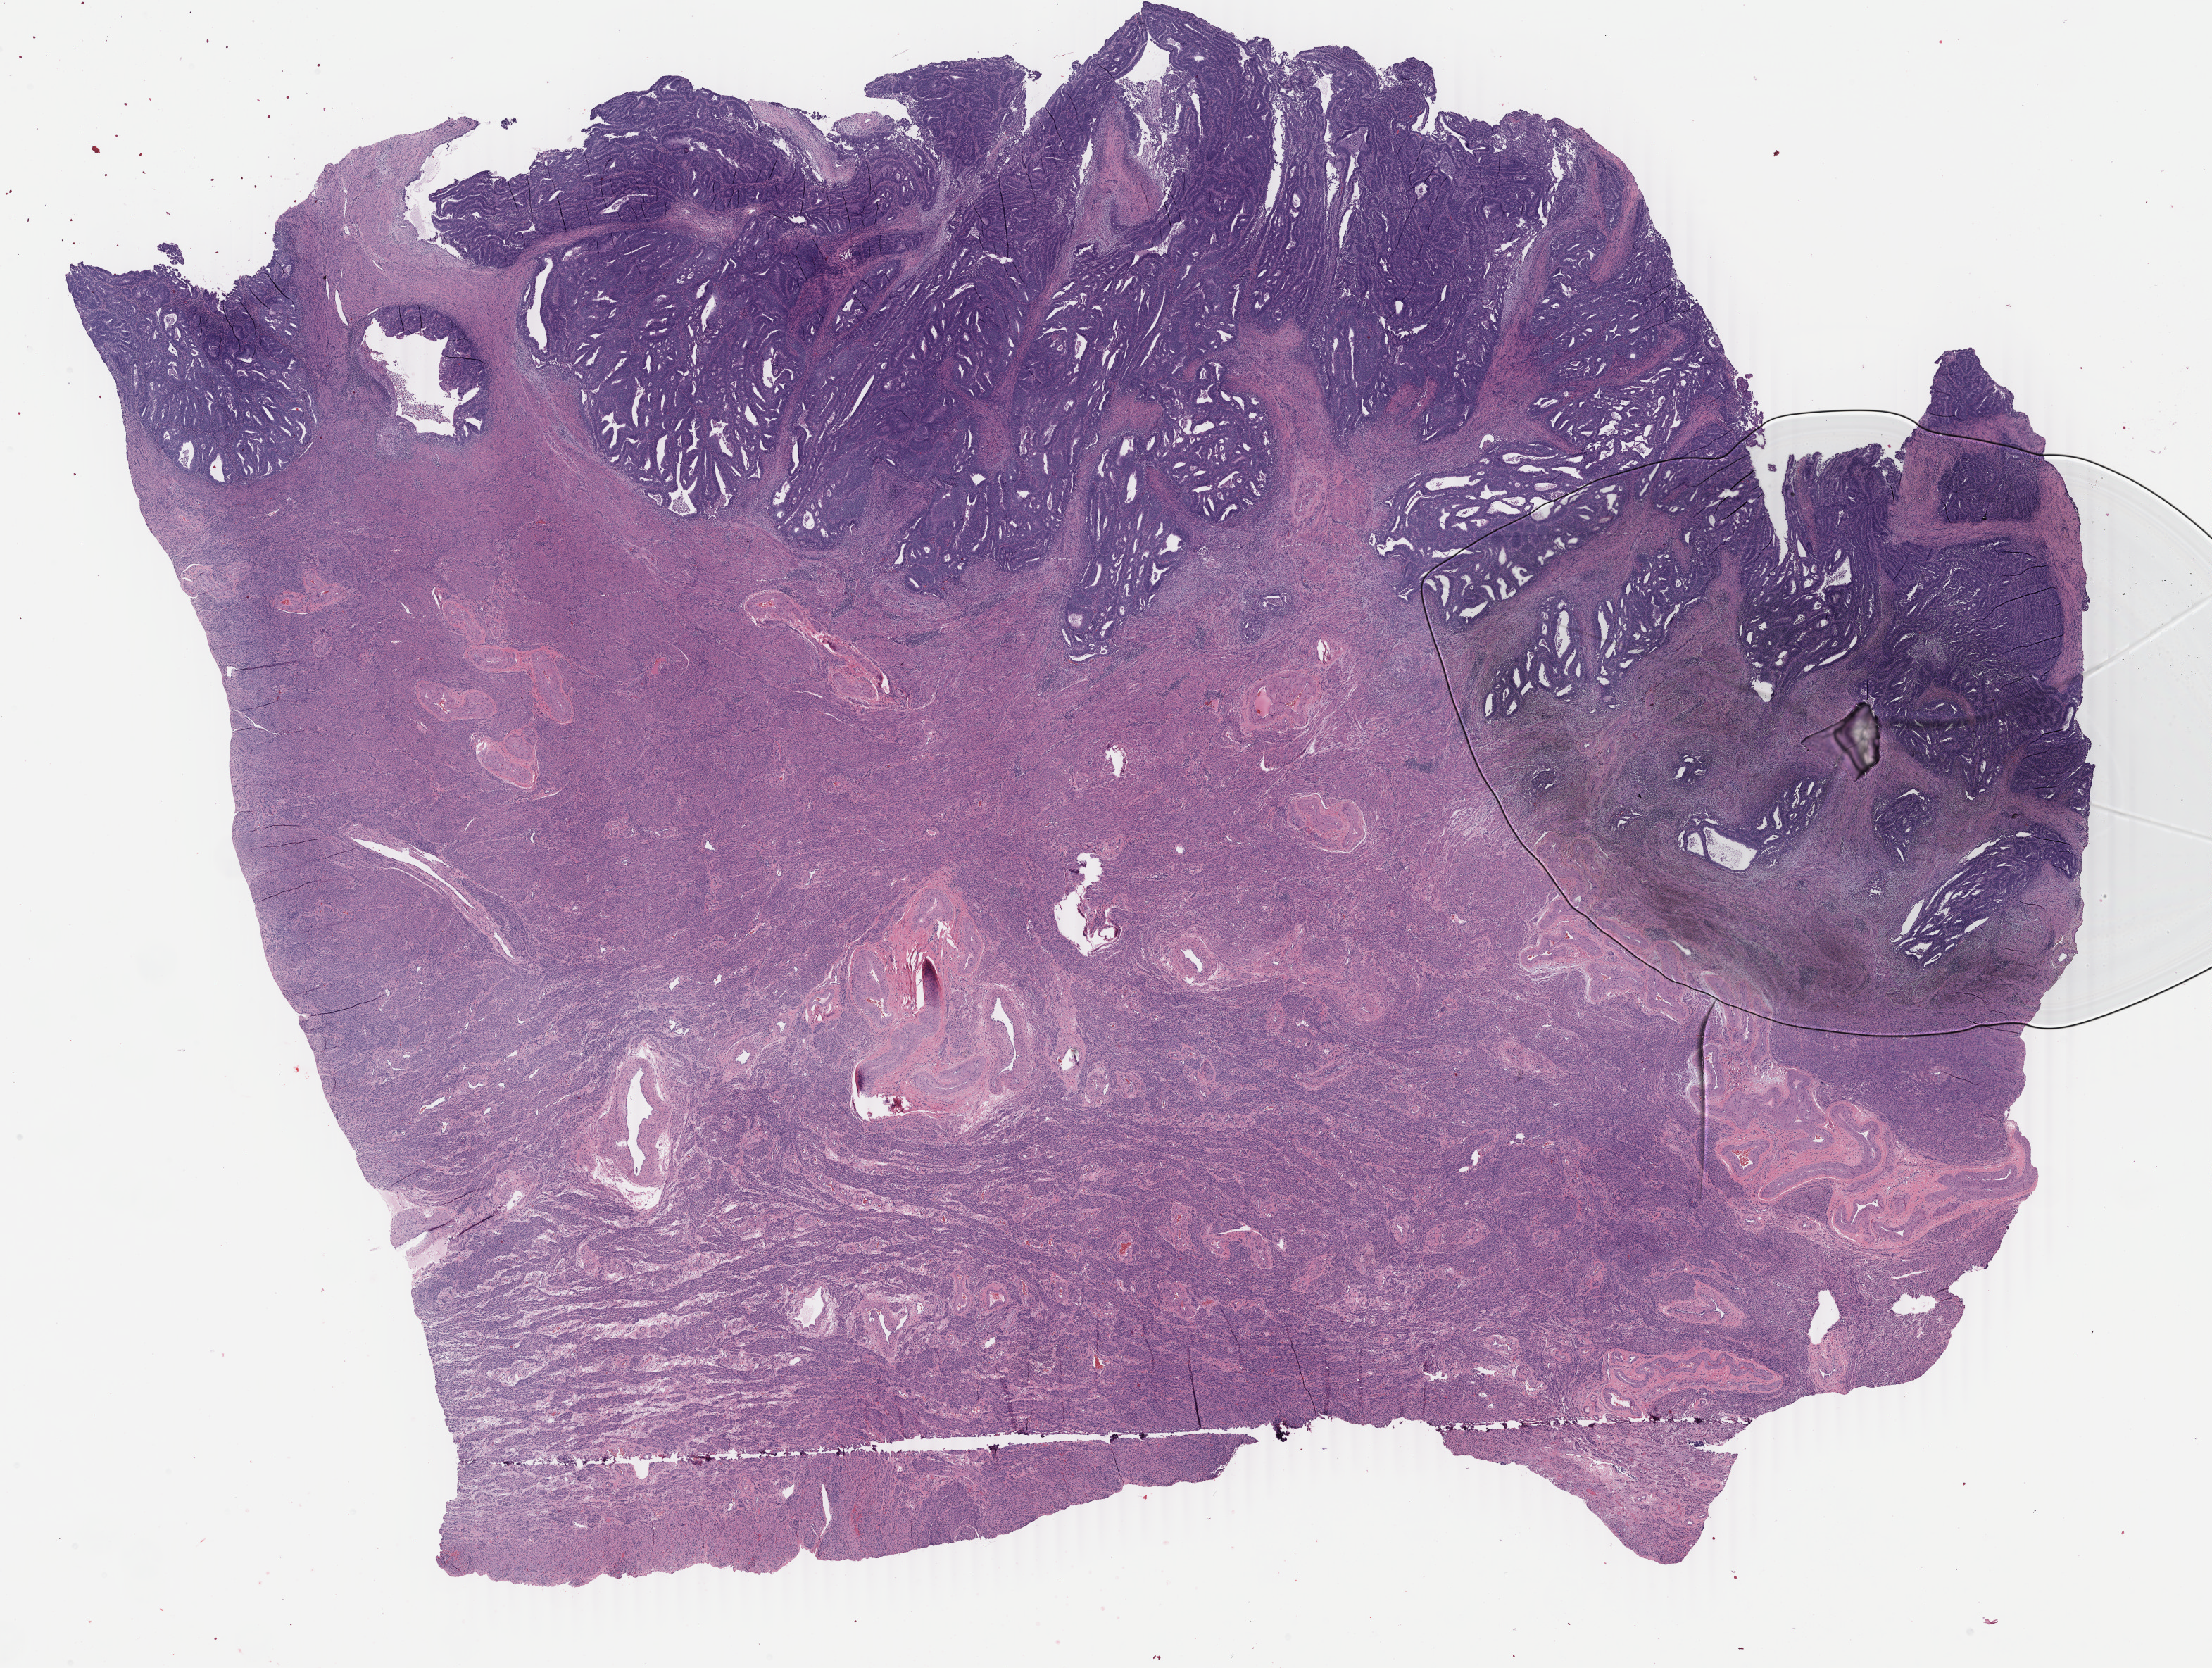
Digitized Hematoxylin and eosin (H&E) stained tissue section (whole slide), whole scanned area (about 25.0 x 18.8 mm) shown as a low-resolution overview, FFPE section, sample: primary tumour, uterus. Female patient; age at initial diagnosis 65 years. Histologic grade: G2 (moderately differentiated).
- FIGO stage: IB
- diagnosis: Endometrioid adenocarcinoma, NOS